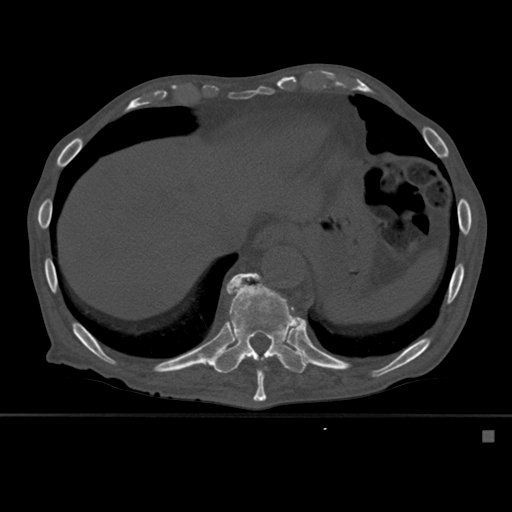
CT including the spine, one axial slice; position 303 of 527 along the scan axis; bone window (W 1800 / L 400 HU); 1.5 mm slice thickness; 512 × 512 image matrix, field of view 373 × 373 mm. Male patient, age 78 years. From the clinical record (not read from this slice): primary cancer: prostate.
Outlined on this slice (semi-automatic segmentation, software-assisted and operator-edited):
- T10 vertebra: bounding box (x1, y1, x2, y2) in pixels: (231, 273, 293, 402)
- T11 vertebra: (211, 272, 310, 374)